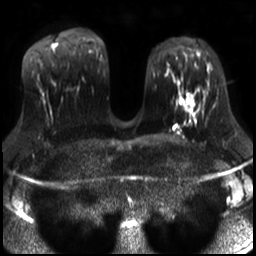
Breast MRI, one axial slice. Position 15 of 30 along the scan axis. Diffusion-weighted series; image 2 of 4 stored at this slice position (different b-values; order by instance number). 3 T. 4 mm slice thickness. 256 × 256 image matrix, field of view 320 × 320 mm. Female patient.
Annotated regions visible in this slice (outlined manually by an expert reader):
- tumour on diffusion-weighted imaging: bounding box [x1, y1, x2, y2] px = [181, 93, 194, 111]